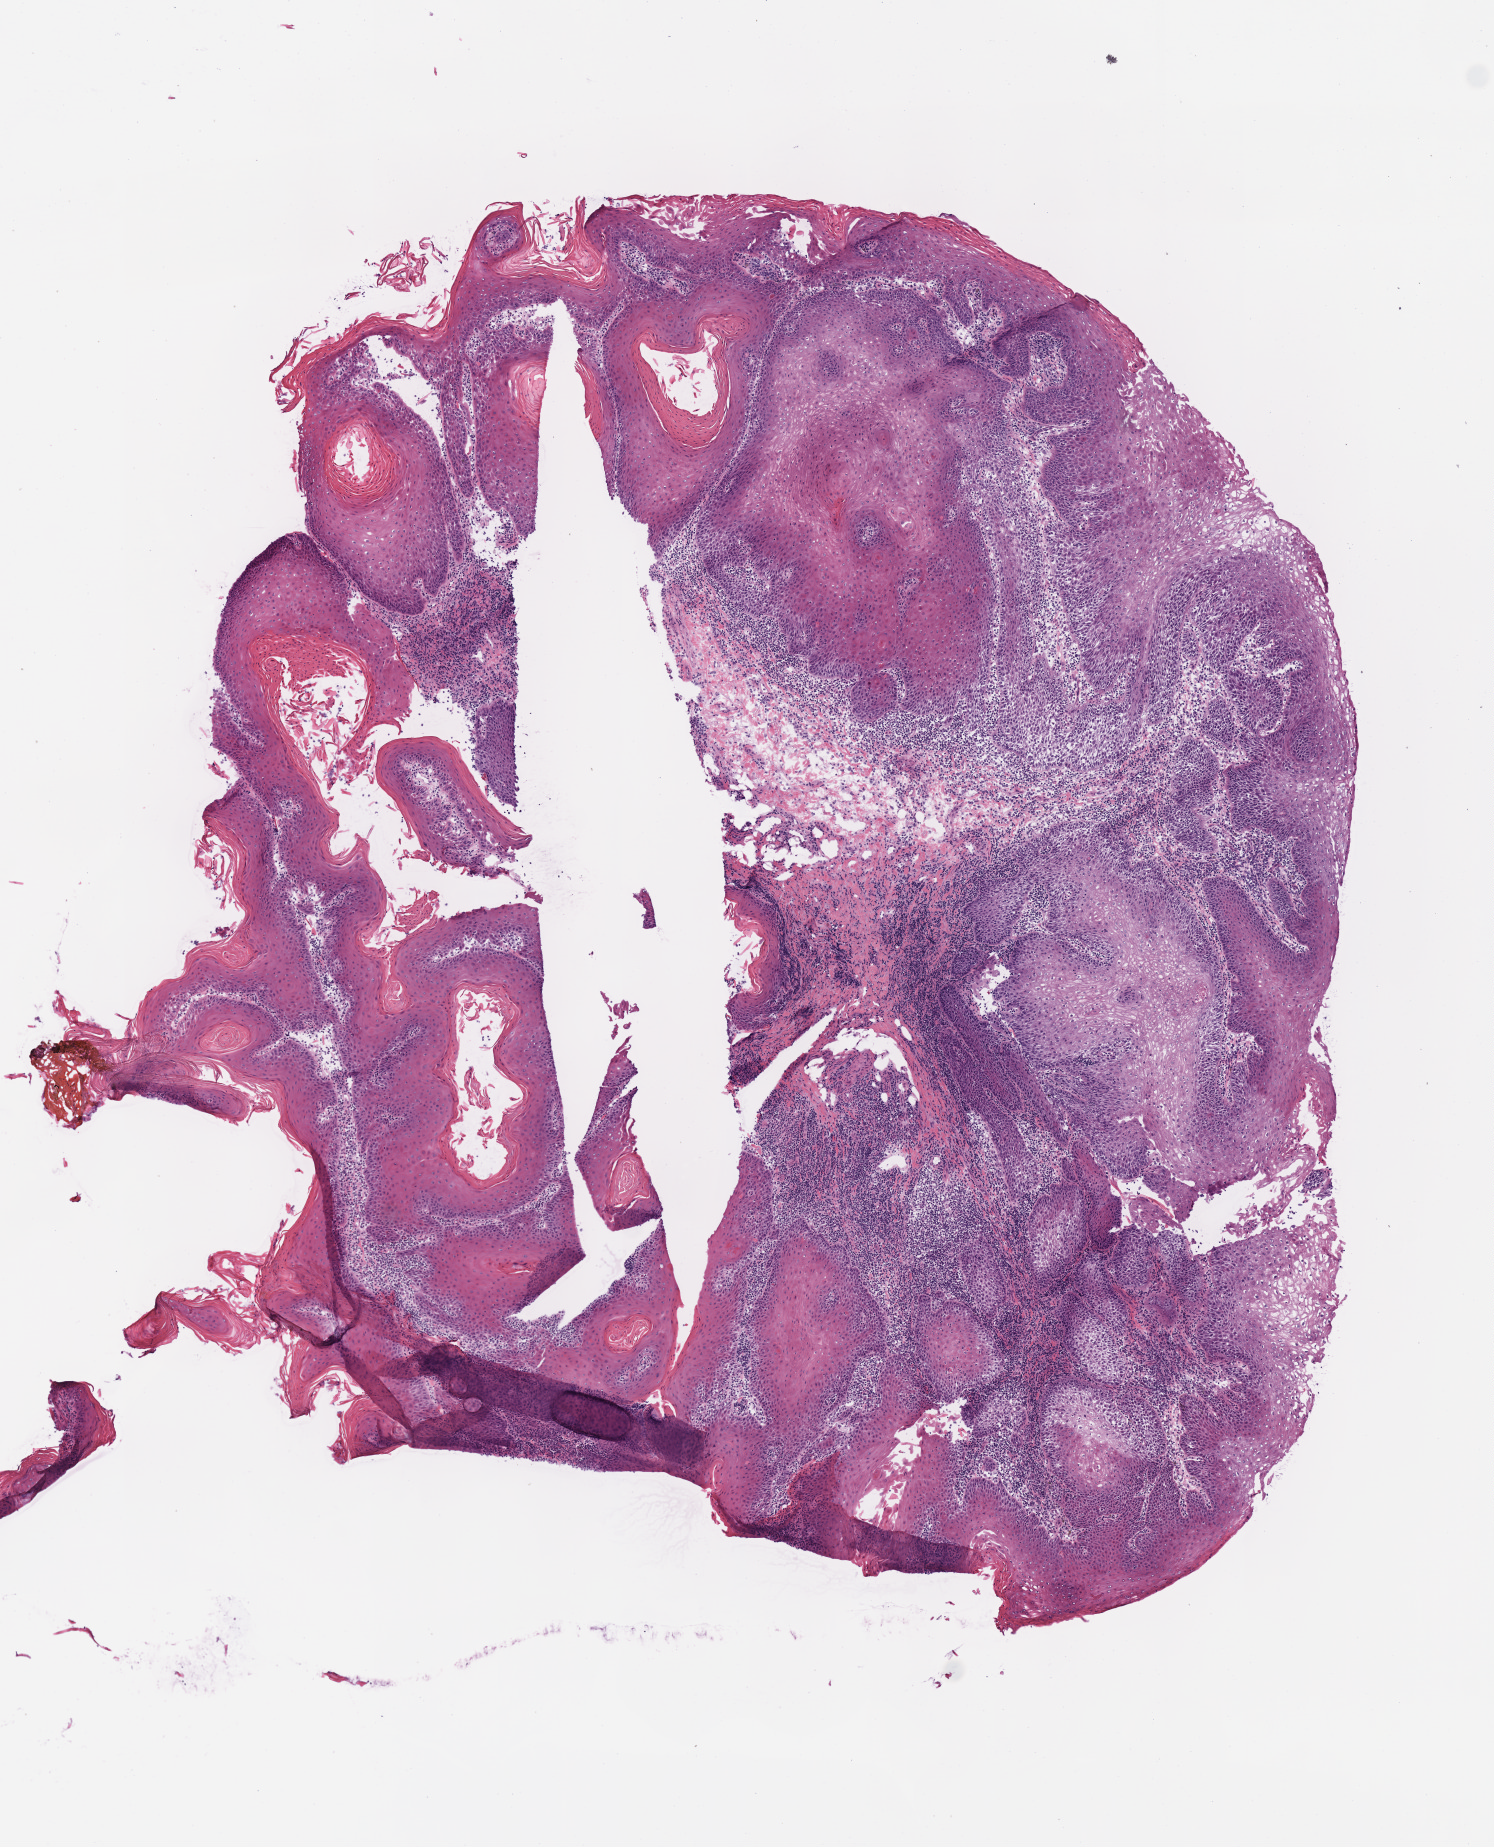
Whole-slide histology image, Hematoxylin and eosin (H&E) stained — whole scanned area (about 5.9 x 7.3 mm) shown as a low-resolution overview, frozen section, head and neck, primary tumour sample. Female, age 75 years at initial diagnosis. Histologic grade: G2 (moderately differentiated). Composition of this section per pathologist review: tumour cells 90%, tumour nuclei 65%, normal cells 0%, stromal cells 10%, necrosis 0%. Inflammatory infiltration, as recorded: lymphocyte infiltration 25%, monocyte infiltration 0%, neutrophil infiltration 1%.
* histologic diagnosis: Squamous cell carcinoma, NOS (overlapping lesion of lip, oral cavity and pharynx)
* TNM: T4a N0
* AJCC pathologic stage: IVA